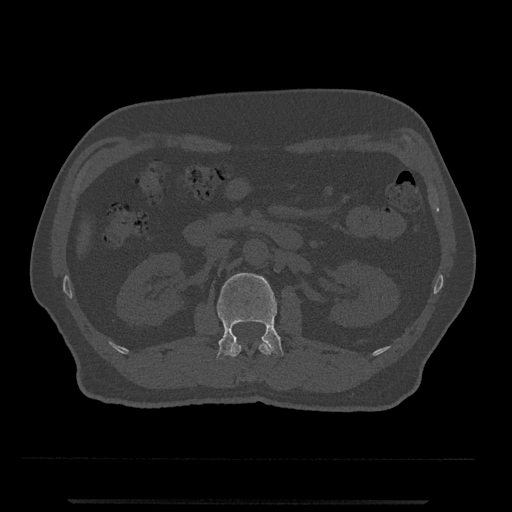
CT including the spine, one axial slice. Slice 287 of 797 in the series (ordered by position). Reconstruction kernel Br40s/3. Bone window (W 1800 / L 400 HU). 0.5 mm slice thickness. 512 × 512 image matrix. Male patient, age 63 years. Case-level facts recorded for this patient, not image findings: primary cancer: prostate.
Annotated regions visible in this slice (semi-automatic segmentation, software-assisted and operator-edited):
- L1 vertebra: bounding box (x1, y1, x2, y2) in pixels: (231, 341, 273, 357)
- L2 vertebra: (217, 273, 284, 359)